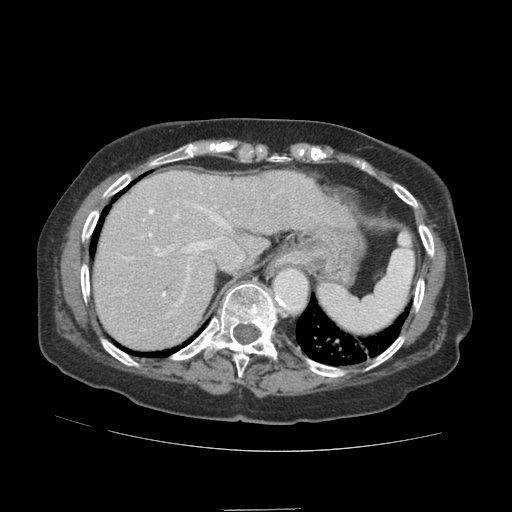
Contrast-enhanced abdominal CT (liver protocol), one axial slice; position 71 of 89 along the scan axis; 140 kVp; soft-tissue window (W 400 / L 40 HU); 2.5 mm slice thickness; 512 × 512 image matrix. From the clinical record (not read from this slice): diagnosis: hepatocellular carcinoma (patient treated with transarterial chemoembolisation; whether this scan precedes or follows treatment is not stated here); TNM stage (as recorded): Stage-II; Child-Pugh class: A; tumour differentiation: moderately differentiated; tumour nodularity: multinodular.
Annotated regions visible in this slice (semi-automatically segmented with operator editing):
- abdominal aorta: bounding box [x1, y1, x2, y2] px = [275, 270, 308, 310]
- liver parenchyma outside the tumour (the mass and vessels are separate outlines, so this box may not span the whole liver): [94, 170, 344, 348]
- liver vessels: [123, 192, 242, 313]